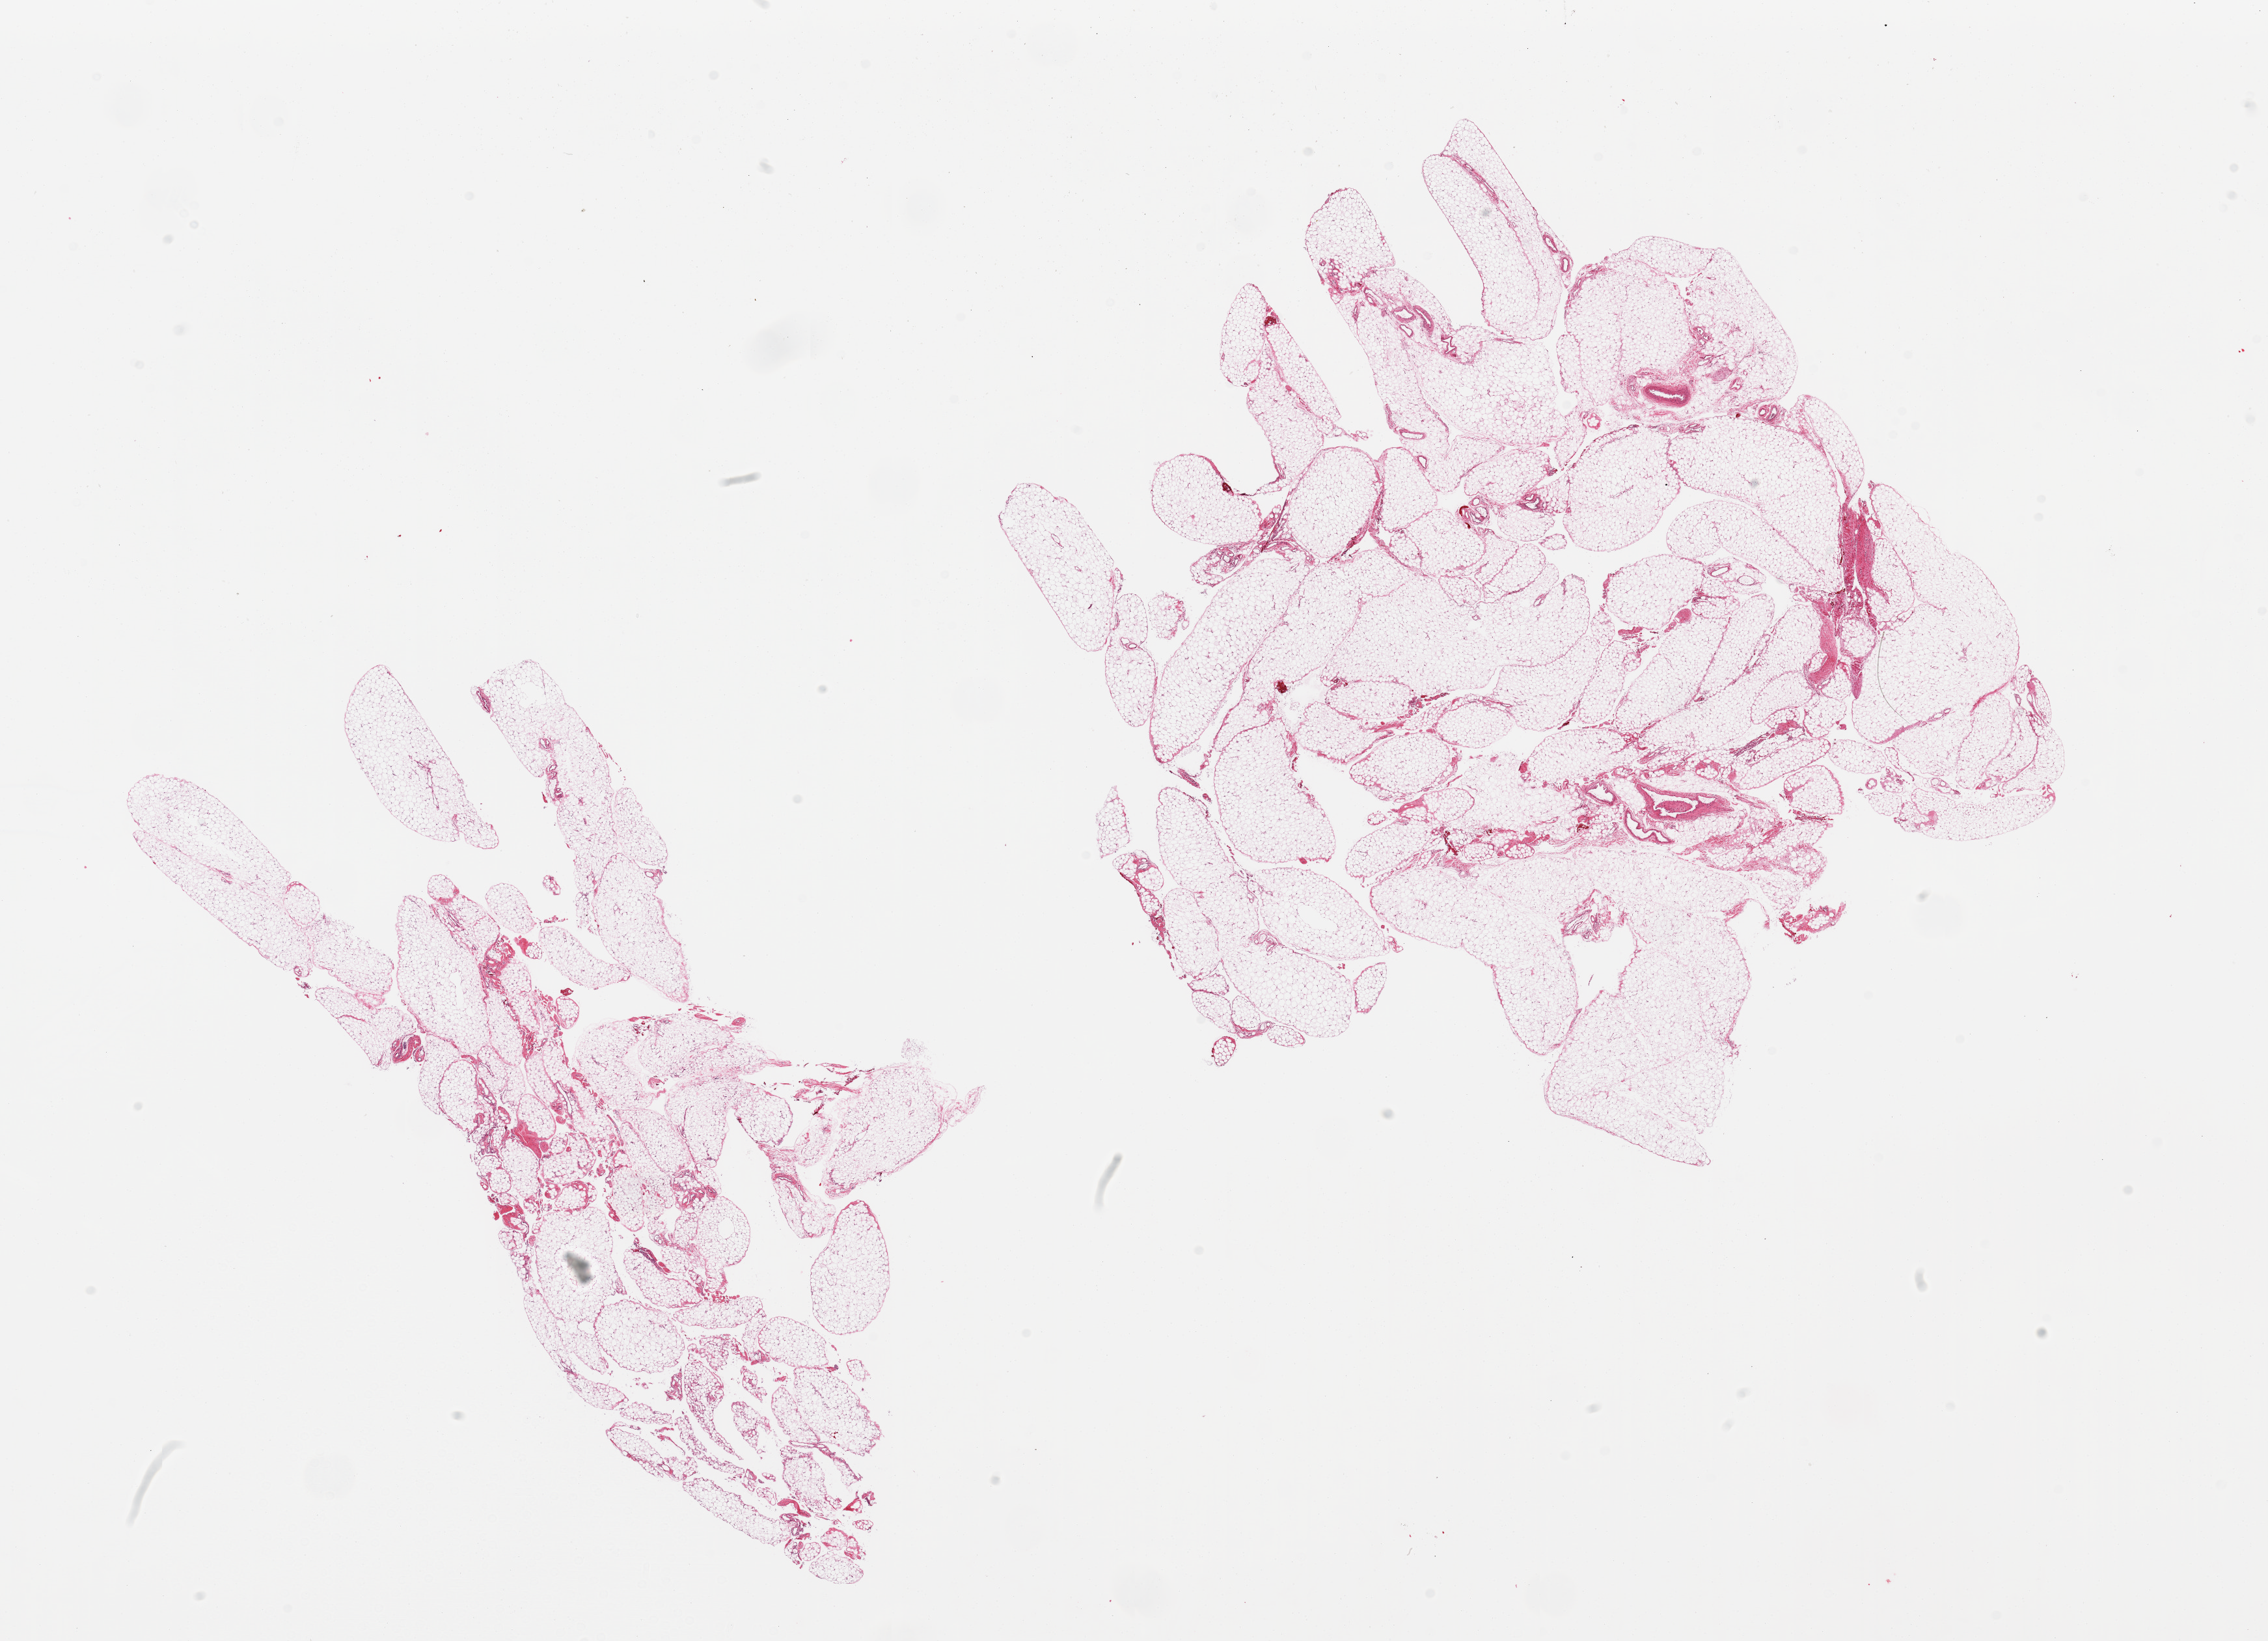
Whole-slide image, haematoxylin and eosin stain — a low-resolution overview of the entire scanned area, about 27.6 x 19.9 mm, PAXgene-fixed paraffin-embedded (PFPE) section, target tissue: omentum, donor tissue sample. Female donor.
* pathologist's review note for this sample: 2 pieces, minimal fibrosis